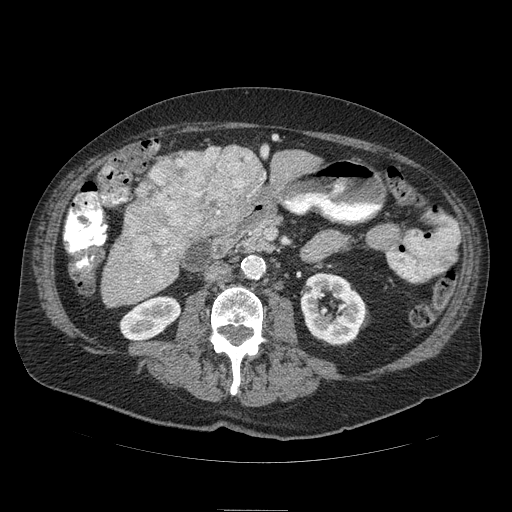
Contrast-enhanced abdominal CT (liver protocol), one axial slice. Position 24 of 103 along the scan axis. 120 kVp. Soft-tissue window (W 400 / L 40 HU). 2.5 mm slice thickness. 512 × 512 image matrix, field of view 440 × 440 mm. Case-level facts recorded for this patient, not image findings: diagnosis: hepatocellular carcinoma (patient treated with transarterial chemoembolisation; whether this scan precedes or follows treatment is not stated here); TNM stage (as recorded): Stage-IIIA; Child-Pugh class: B; tumour differentiation: well differentiated; tumour nodularity: multinodular.
Structures marked on this image (semi-automatically segmented with operator editing):
- liver parenchyma outside the tumour (the mass and vessels are separate outlines, so this box may not span the whole liver): bounding box [x1, y1, x2, y2] px = [110, 144, 320, 278]
- mass: [126, 144, 269, 268]
- liver vessels: [263, 150, 267, 155]